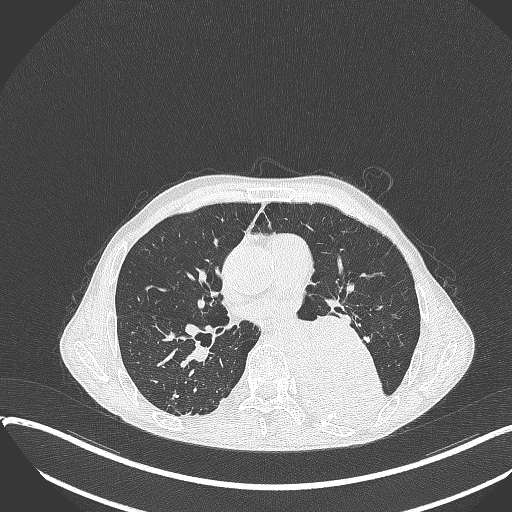
Chest CT, one axial slice. Position 191 of 401 along the scan axis. Lung window (W 1500 / L -600 HU). 1 mm slice thickness. 512 × 512 image matrix, field of view 400 × 400 mm. Patient: male, 57 years. From the clinical record (not read from this slice): clinical TNM (as recorded): T4 N0 M0.
Structures marked on this image (rectangle marked by the reading radiologist):
- lung tumour (recorded histology: squamous cell carcinoma): bounding box (x1, y1, x2, y2) in pixels: (286, 315, 384, 425)